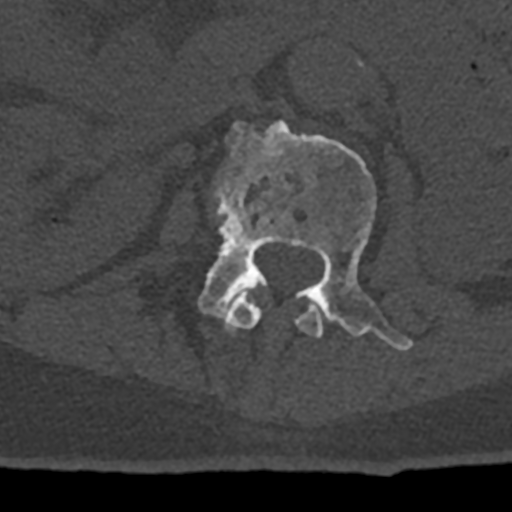
CT including the spine, one axial slice. Position 393 of 797 along the scan axis. Reconstruction kernel Br40s/3. Bone window (W 1800 / L 400 HU). 512 × 512 image matrix, field of view 160 × 160 mm. Male patient, age 74 years. Case-level facts recorded for this patient, not image findings: primary cancer: renal; vertebrae with lytic lesions (as recorded): T10, L1, L2, L3, L4, L5.
Structures marked on this image (semi-automatic segmentation, software-assisted and operator-edited):
- L1 vertebra: bounding box <225,288,323,337> (left, top, right, bottom; pixels)
- L2 vertebra: <198,121,413,351>